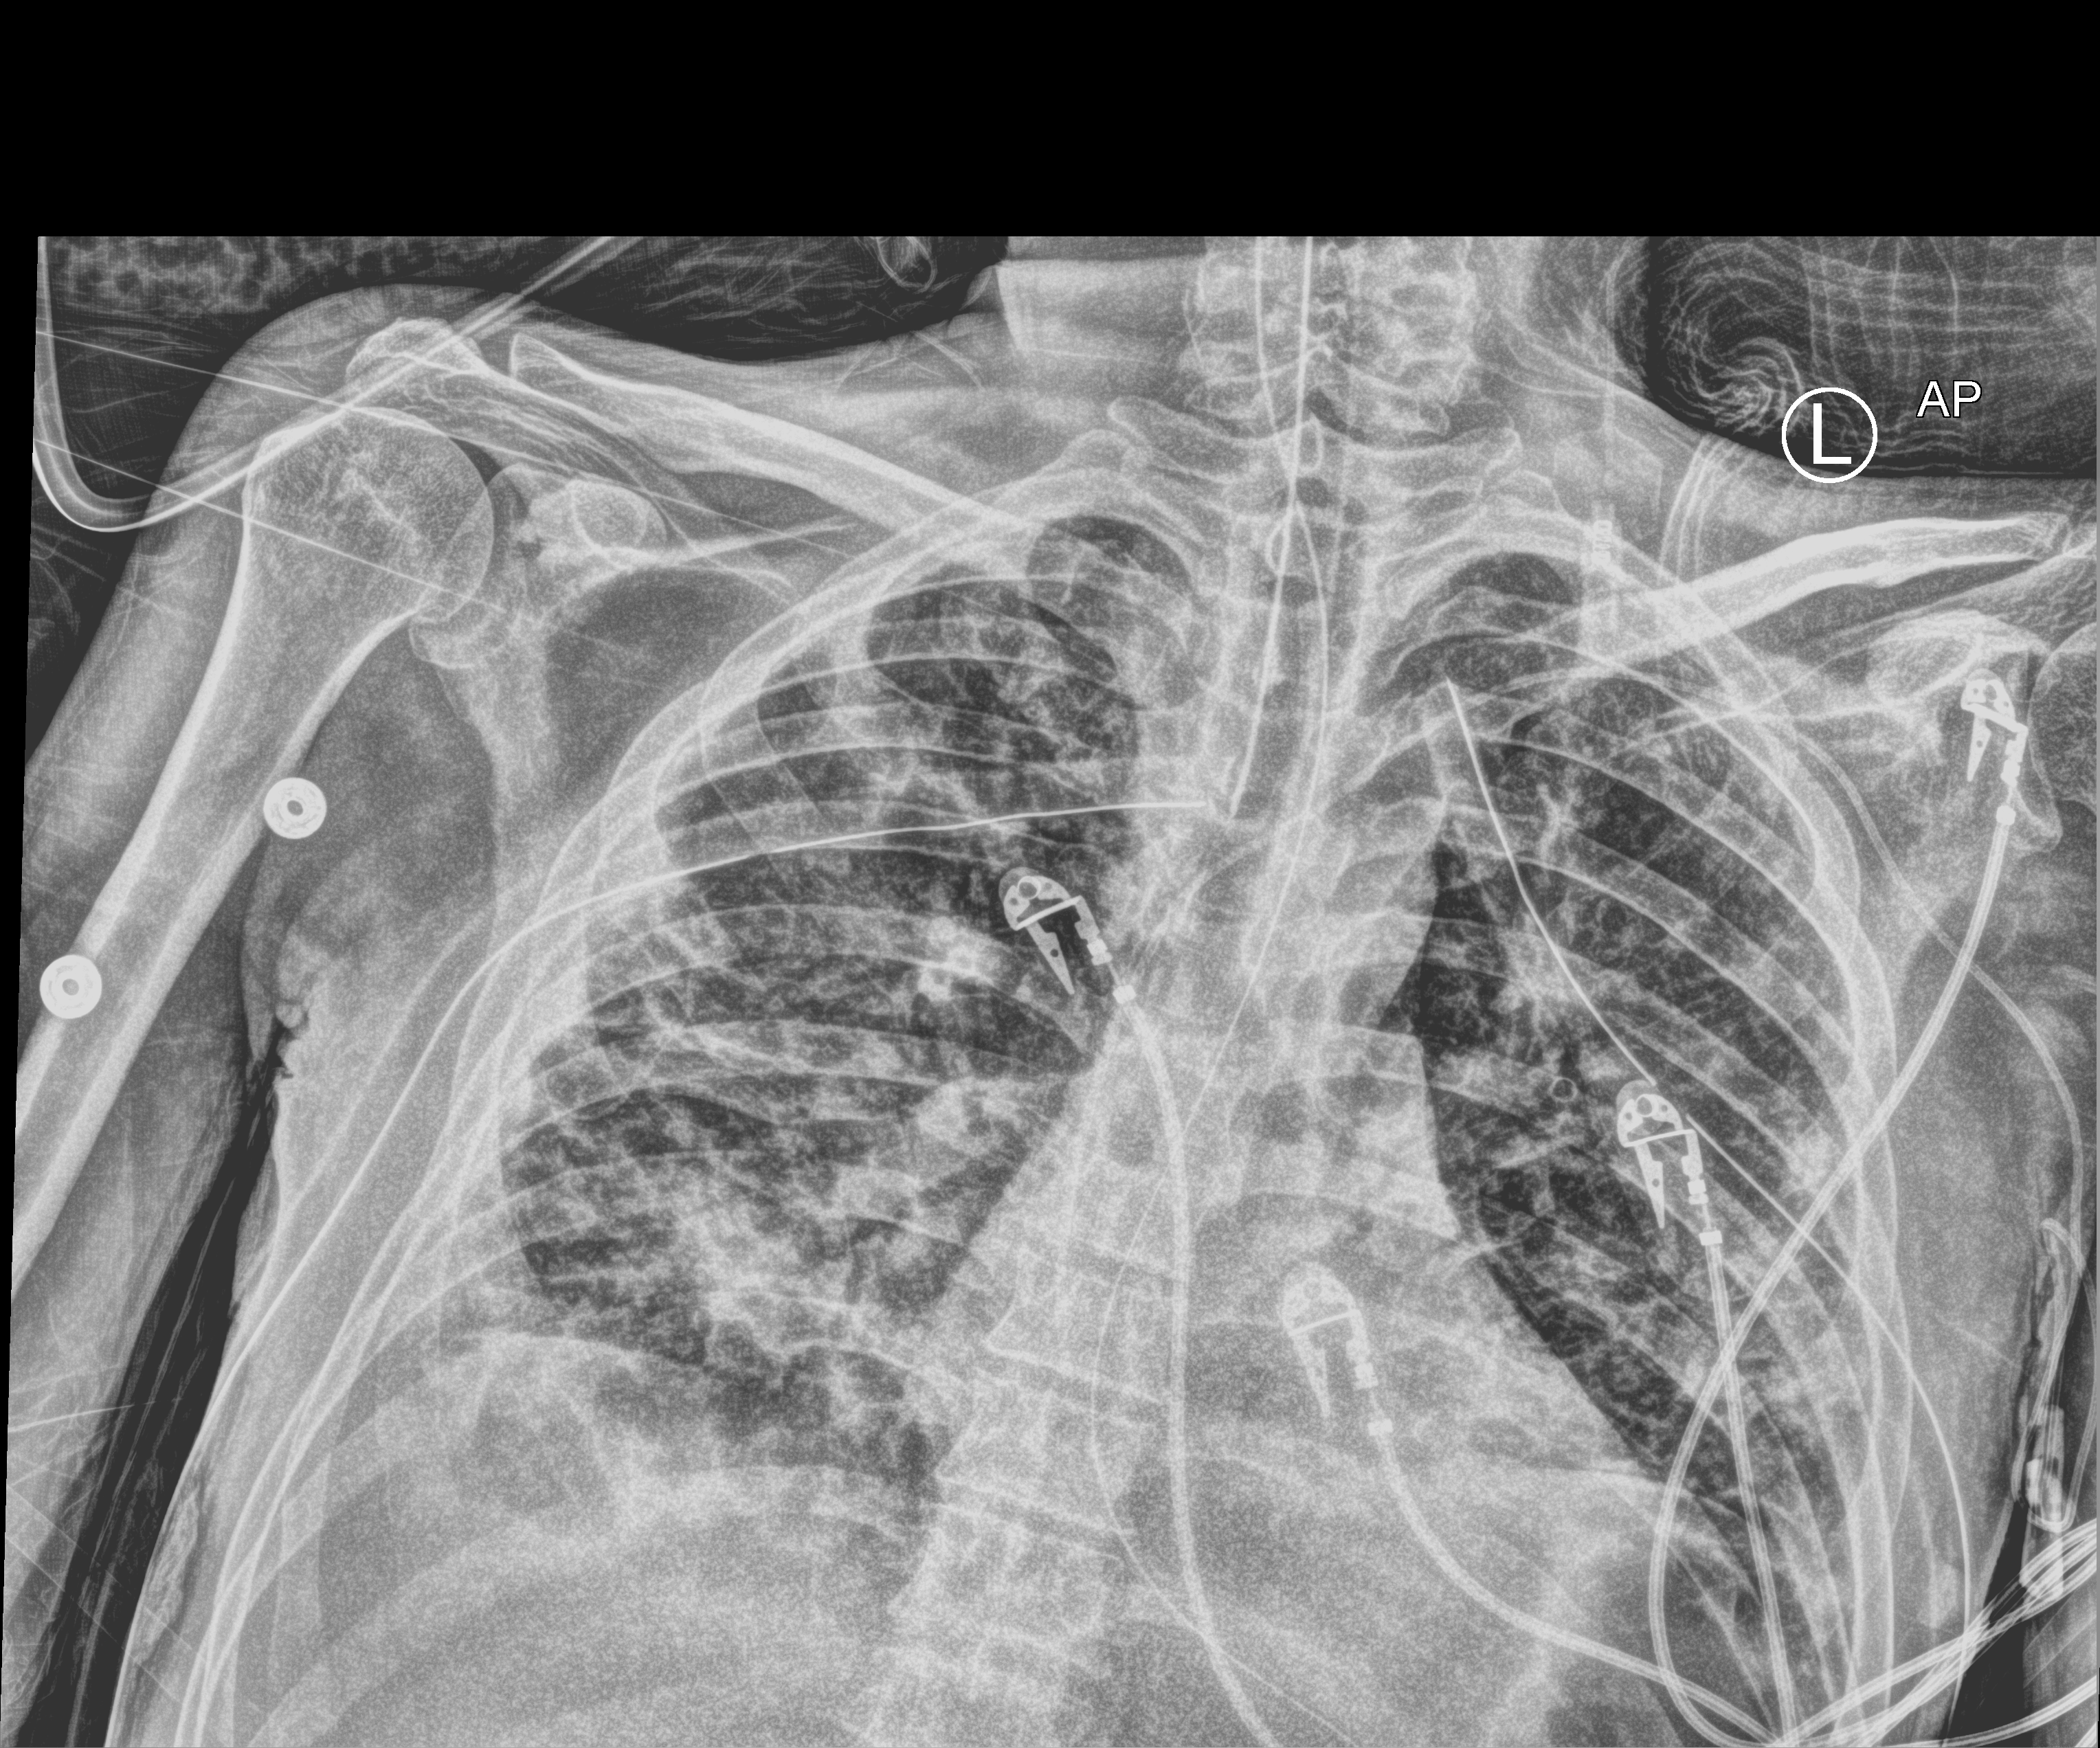
Bedside chest radiograph (computed radiography). Patient hospitalised with COVID-19; male, aged 18–59 years.
Admission-level facts for this patient (not findings on this image; timing relative to this image not recorded):
- chronic kidney disease (admission record): no
- hypertension (admission record): yes
- smoking status (admission record): never